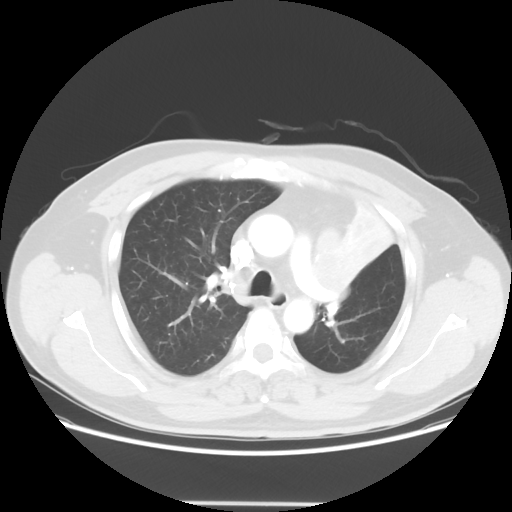
Chest CT, one axial slice; reconstruction kernel STANDARD; lung window (W 1500 / L -600 HU); 512 × 512 image matrix, field of view 403 × 403 mm. Male patient, age 49 years. From the clinical record (not read from this slice): clinical TNM (as recorded): T3 N3 M1c.
Outlined on this slice (rectangle marked by the reading radiologist):
- lung tumour (recorded histology: squamous cell carcinoma): box from (x=307, y=229) to (x=347, y=305) px